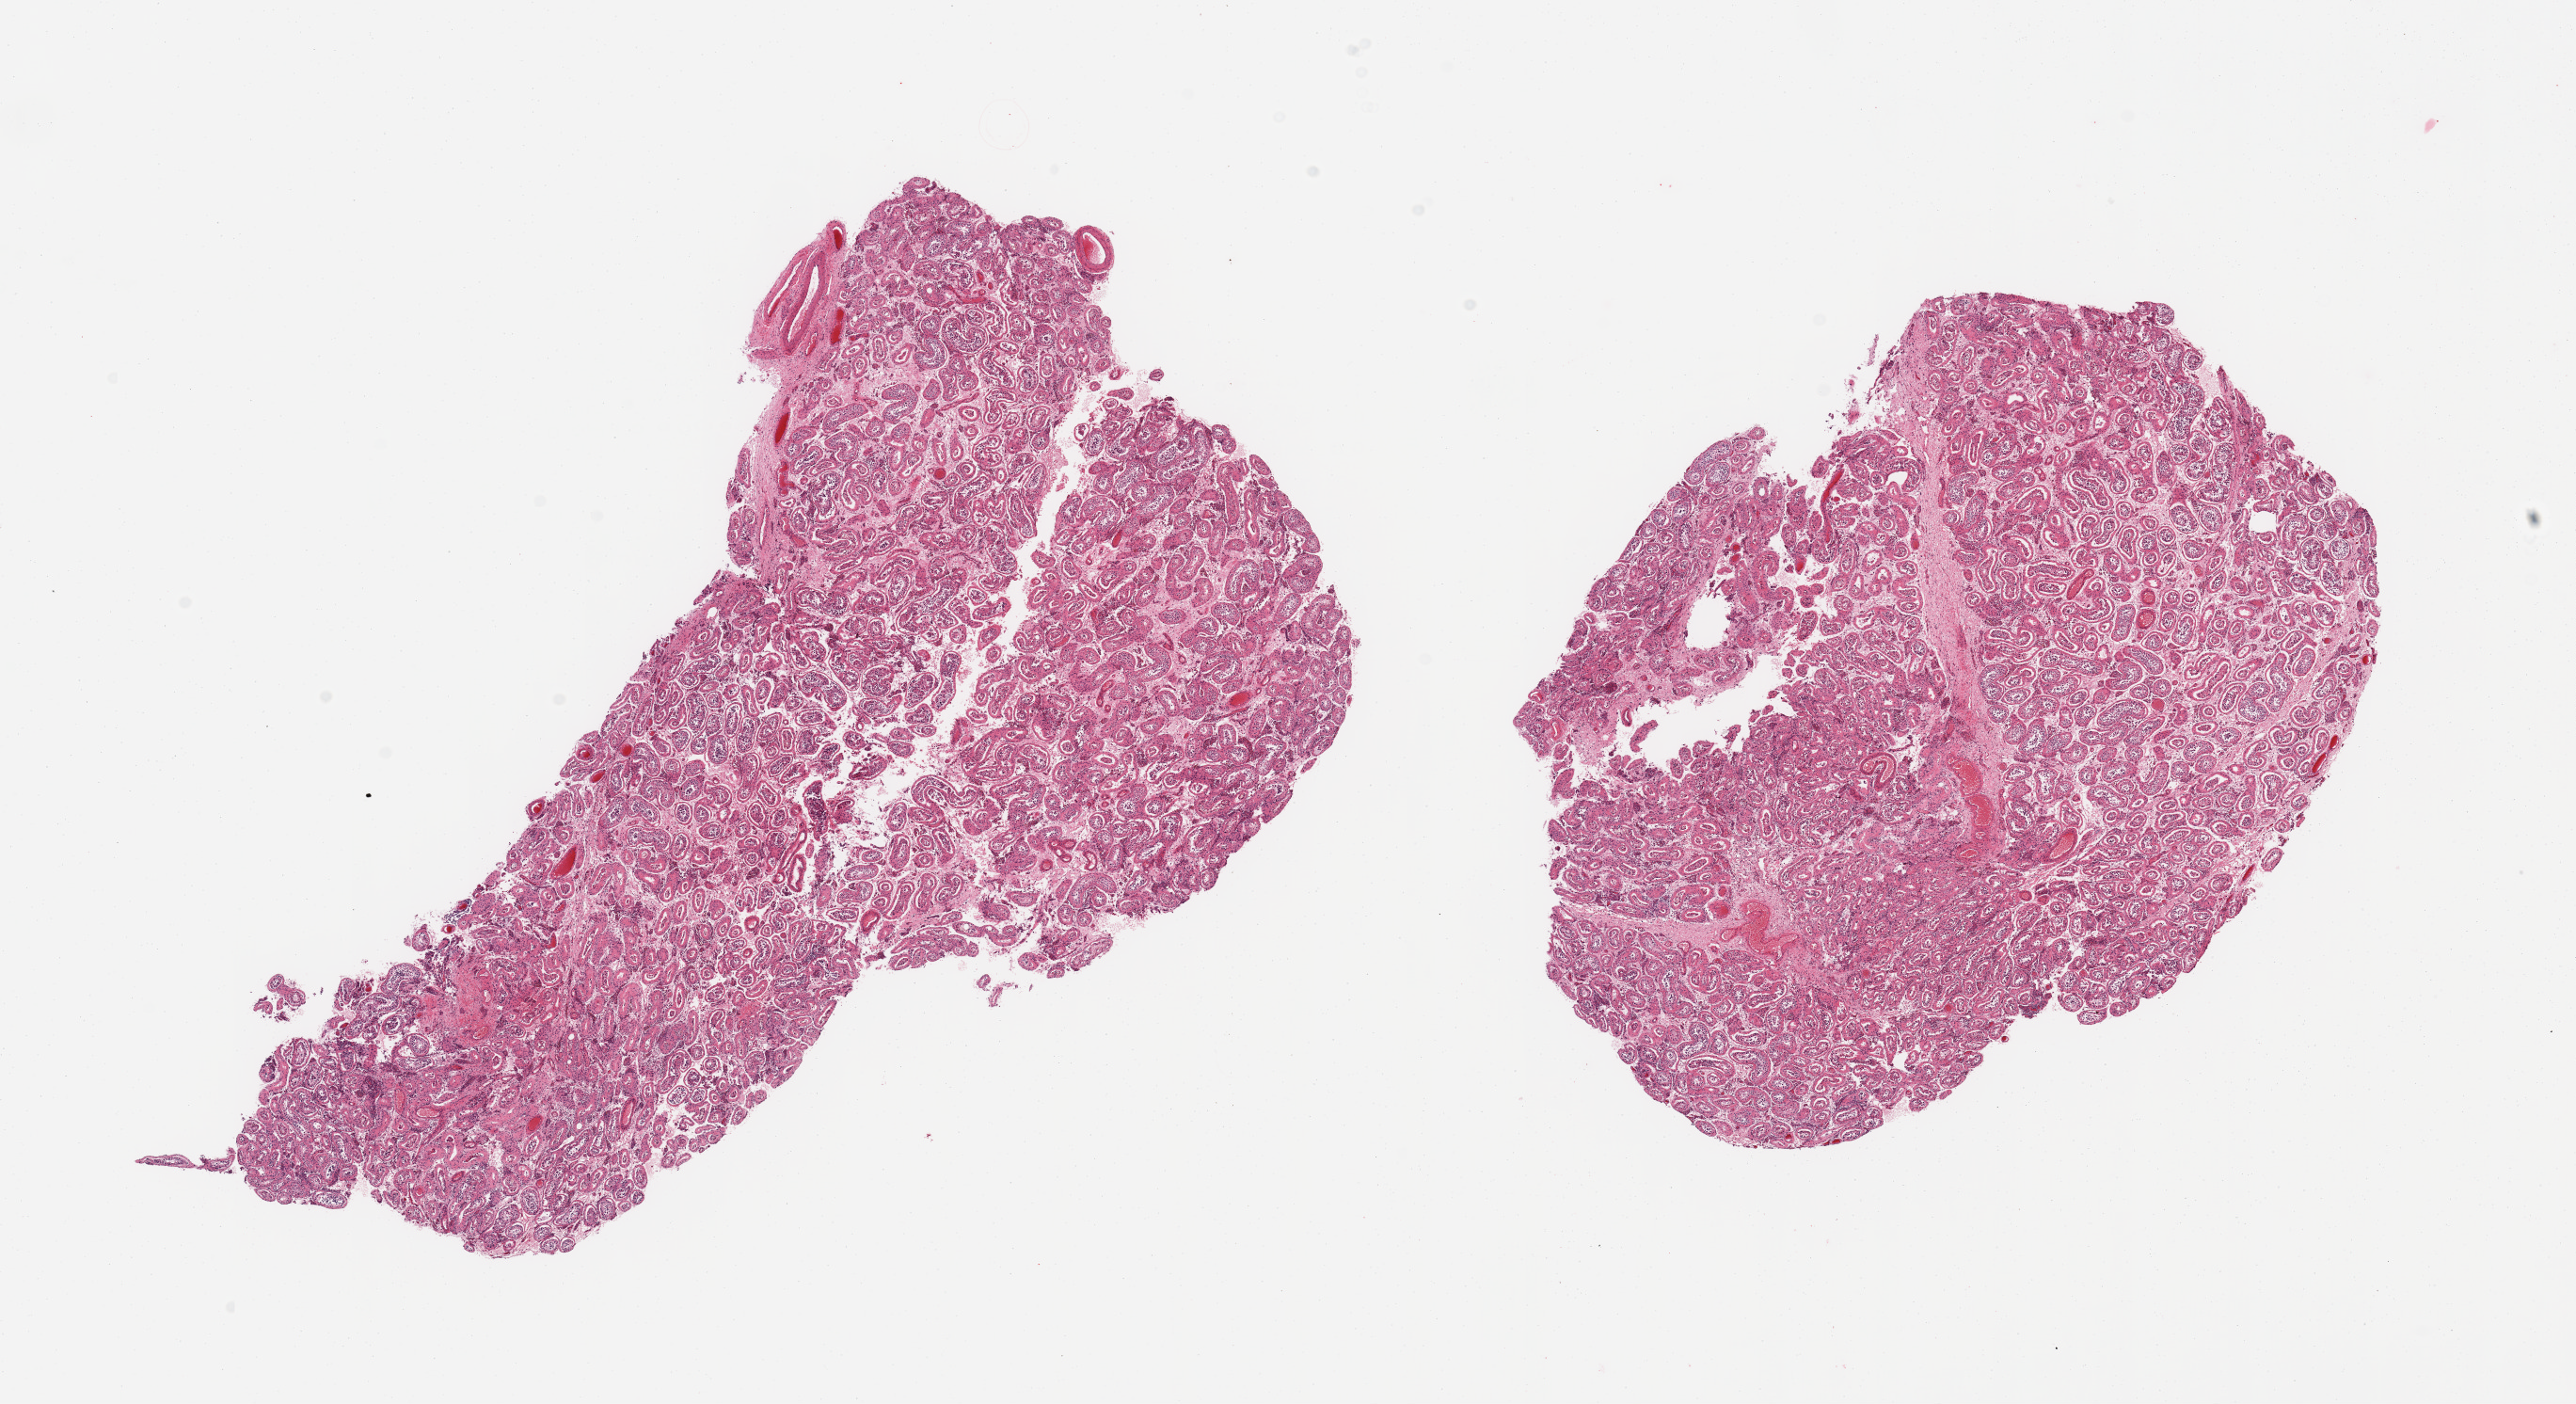
Digitized hematoxylin and eosin (H&E)-stained section, brightfield — a low-resolution overview of the entire scanned area, about 21.7 x 11.8 mm (slide scanned at 20x), PAXgene-fixed, paraffin-embedded tissue, target tissue: testis, tissue donor sample. Male donor.
Reviewer comment on this tissue sample: 2 pieces. Spermatogenesis appears reduced.